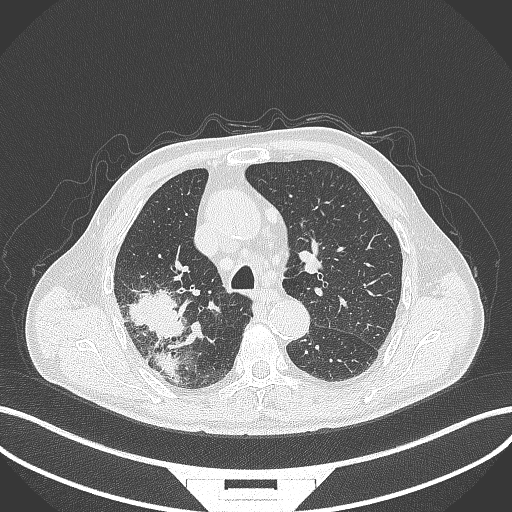
Chest CT, one axial slice. Reconstruction kernel B70f. Lung window (W 1500 / L -600 HU). 1 mm slice thickness. 512 × 512 image matrix. Patient: male, 72 years. From the clinical record (not read from this slice): clinical TNM (as recorded): T3 N2 M0.
Annotated regions visible in this slice (rectangle marked by the reading radiologist):
- lung tumour (recorded histology: adenocarcinoma): bounding box (x1, y1, x2, y2) in pixels: (125, 282, 188, 342)